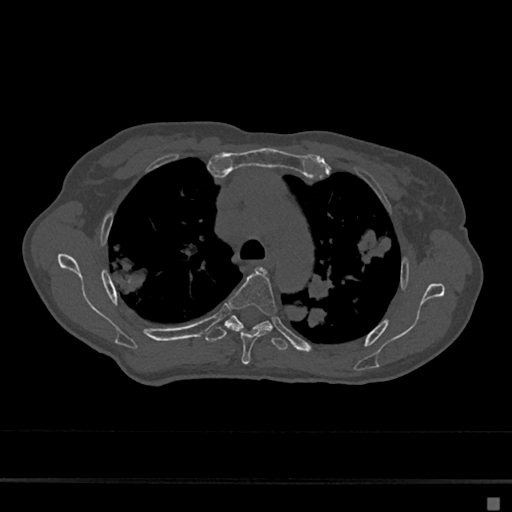
CT including the spine, one axial slice; slice 488 of 797 in the series (ordered by position); 120 kVp; bone window (W 1800 / L 400 HU); 0.5 mm slice thickness; 512 × 512 image matrix, field of view 360 × 360 mm. Patient: female, 68 years. From the clinical record (not read from this slice): primary cancer: renal.
Outlined on this slice (semi-automatic segmentation, software-assisted and operator-edited):
- T4 vertebra: bounding box <227,267,277,365> (left, top, right, bottom; pixels)
- T5 vertebra: <205,315,288,351>